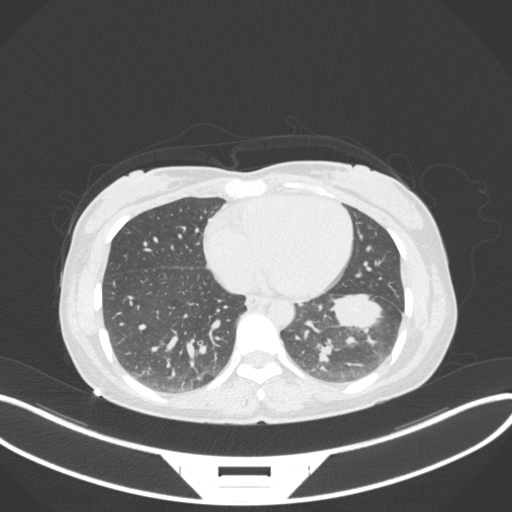
Chest CT, one axial slice; slice 130 of 361 in the series (ordered by position); lung window (W 1500 / L -600 HU); 1 mm slice thickness; 512 × 512 image matrix, field of view 400 × 400 mm. Patient: female, 41 years. From the clinical record (not read from this slice): clinical TNM (as recorded): T2a N3 M1b.
Annotated regions visible in this slice (rectangle marked by the reading radiologist):
- lung tumour (recorded histology: adenocarcinoma): bounding box [x1, y1, x2, y2] px = [325, 289, 384, 330]